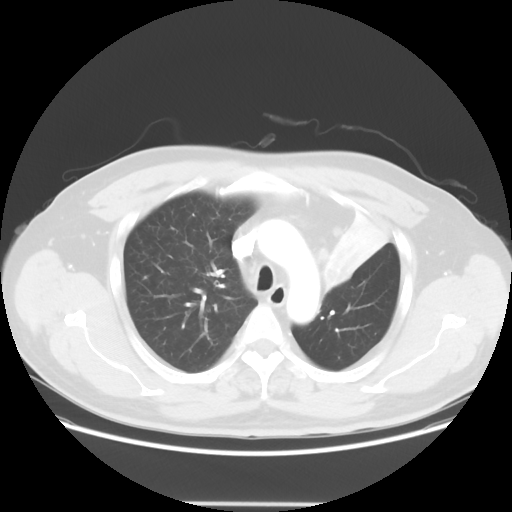
Chest CT, one axial slice; position 45 of 62 along the scan axis; reconstruction kernel STANDARD; lung window (W 1500 / L -600 HU); 5 mm slice thickness; 512 × 512 image matrix, field of view 403 × 403 mm. Male patient, age 49 years. Case-level facts recorded for this patient, not image findings: clinical TNM (as recorded): T3 N3 M1c.
Annotated regions visible in this slice (bounding box drawn by a radiologist):
- lung tumour (recorded histology: squamous cell carcinoma): bounding box <321,252,361,300> (left, top, right, bottom; pixels)